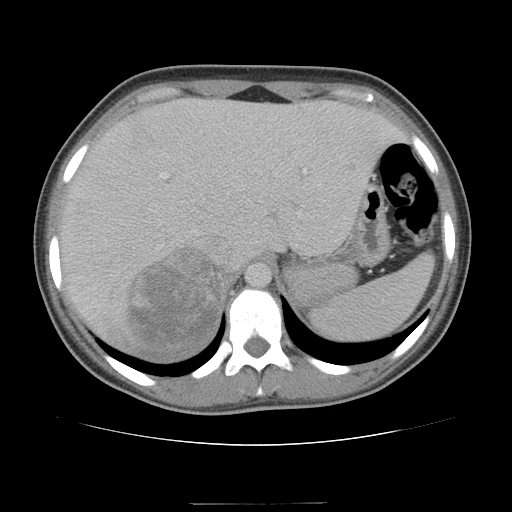
Contrast-enhanced abdominal CT, one axial slice; position 81 of 100 along the scan axis; reconstruction kernel STANDARD; intravenous contrast given; soft-tissue window (W 400 / L 40 HU); 512 × 512 image matrix, field of view 360 × 360 mm. Patient: female, 21 years. Case-level facts recorded for this patient, not image findings: diagnosis: adrenocortical carcinoma; tumour side: right adrenal; tumour size at pathology: 15.5 cm; Ki-67 index: 26 %; stage (as recorded): 3.
Outlined on this slice (semi-automatically segmented with operator editing):
- mass: bounding box [x1, y1, x2, y2] px = [130, 249, 226, 355]